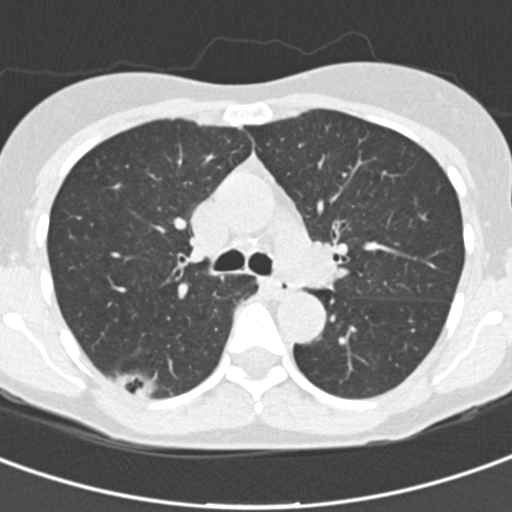
Low-dose screening chest CT, one axial slice; position 101 of 162 along the scan axis; 120 kVp; lung window (W 1500 / L -600 HU); 2 mm slice thickness; 512 × 512 image matrix, field of view 276 × 276 mm.
Structures marked on this image (expert manual segmentation):
- lesion 1 (tumor, lower lobe of right lung): bounding box [x1, y1, x2, y2] px = [137, 382, 154, 397]